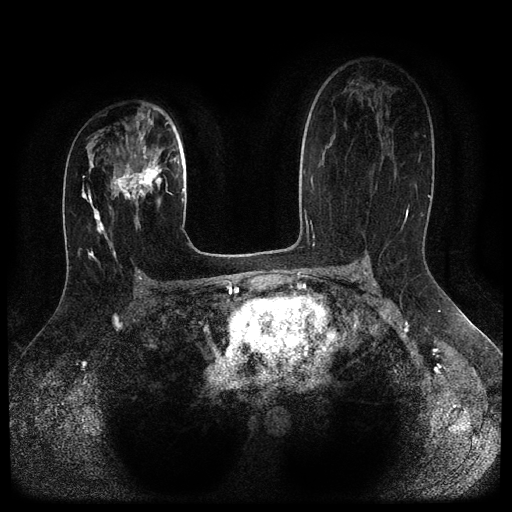
Breast MRI (dynamic contrast-enhanced, multi-phase), one axial slice; dynamic contrast-enhanced series, time point 2 of 5 at this slice position (early post-contrast); 1.5 T; TE 2.6 ms, TR 5.4 ms; 2 mm slice thickness; 512 × 512 image matrix, field of view 340 × 340 mm. Female patient, age 29 years.
Outlined on this slice (semi-automatic segmentation, software-assisted and operator-edited):
- breast lesion (labelled 'tumour' in the annotation; benign lesions carry a separate 'benign' label): bounding box <111,151,172,212> (left, top, right, bottom; pixels)
- breast lesion (labelled benign in the annotation): <93,208,107,237>